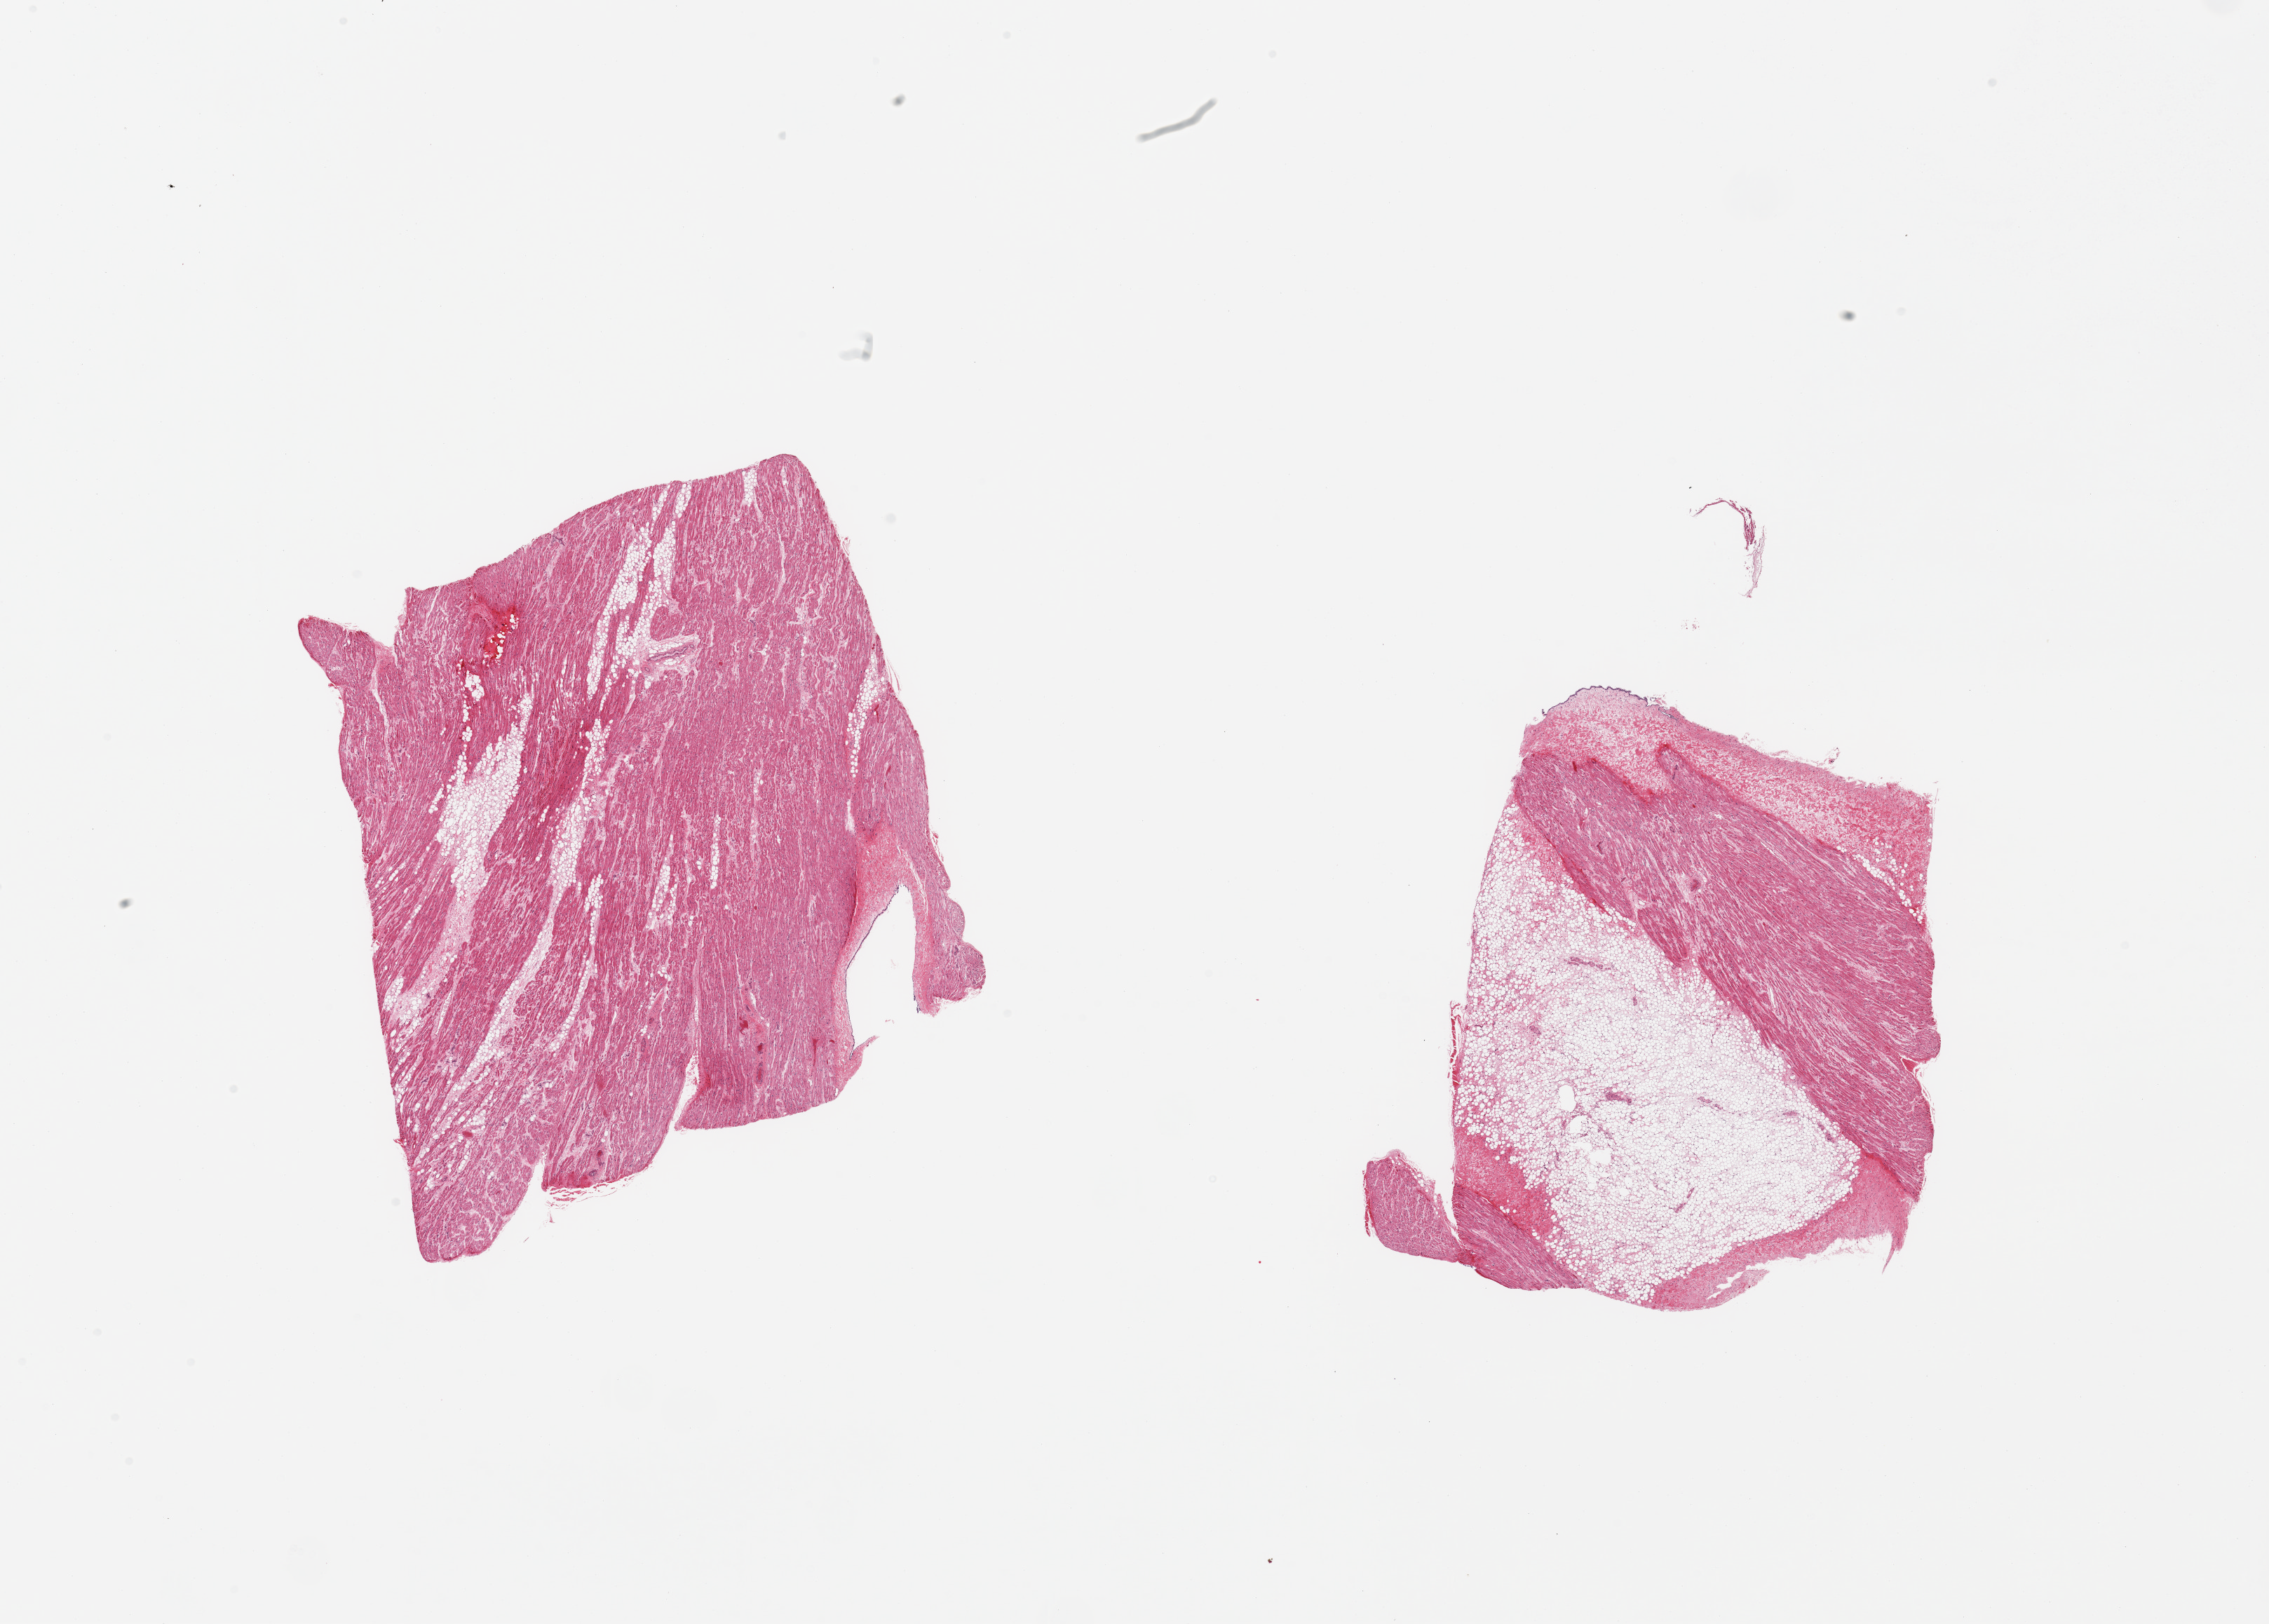
Hematoxylin and eosin (H&E) whole-slide image — a low-resolution overview of the entire scanned area, about 25.6 x 18.3 mm; PAXgene-fixed, paraffin-embedded tissue; section of auricular appendage (target tissue); tissue donor sample. Donor sex: male.
* review note (as recorded): 2 pieces: 1 with 10% internal fat, other with 50% internal; fat